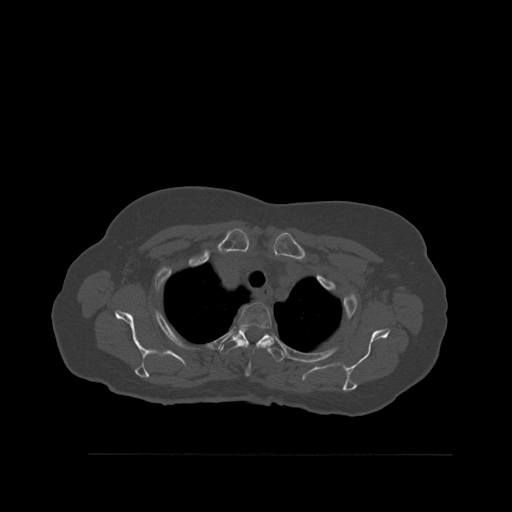
CT including the spine, one axial slice. Position 426 of 527 along the scan axis. Bone window (W 1800 / L 400 HU). 512 × 512 image matrix, field of view 470 × 470 mm. Patient: female, 73 years. From the clinical record (not read from this slice): primary cancer: breast; vertebrae with lytic lesions (as recorded): L2.
Structures marked on this image (semi-automatically segmented with operator editing):
- T2 vertebra: bounding box (x1, y1, x2, y2) in pixels: (235, 303, 272, 377)
- T3 vertebra: (220, 327, 286, 362)